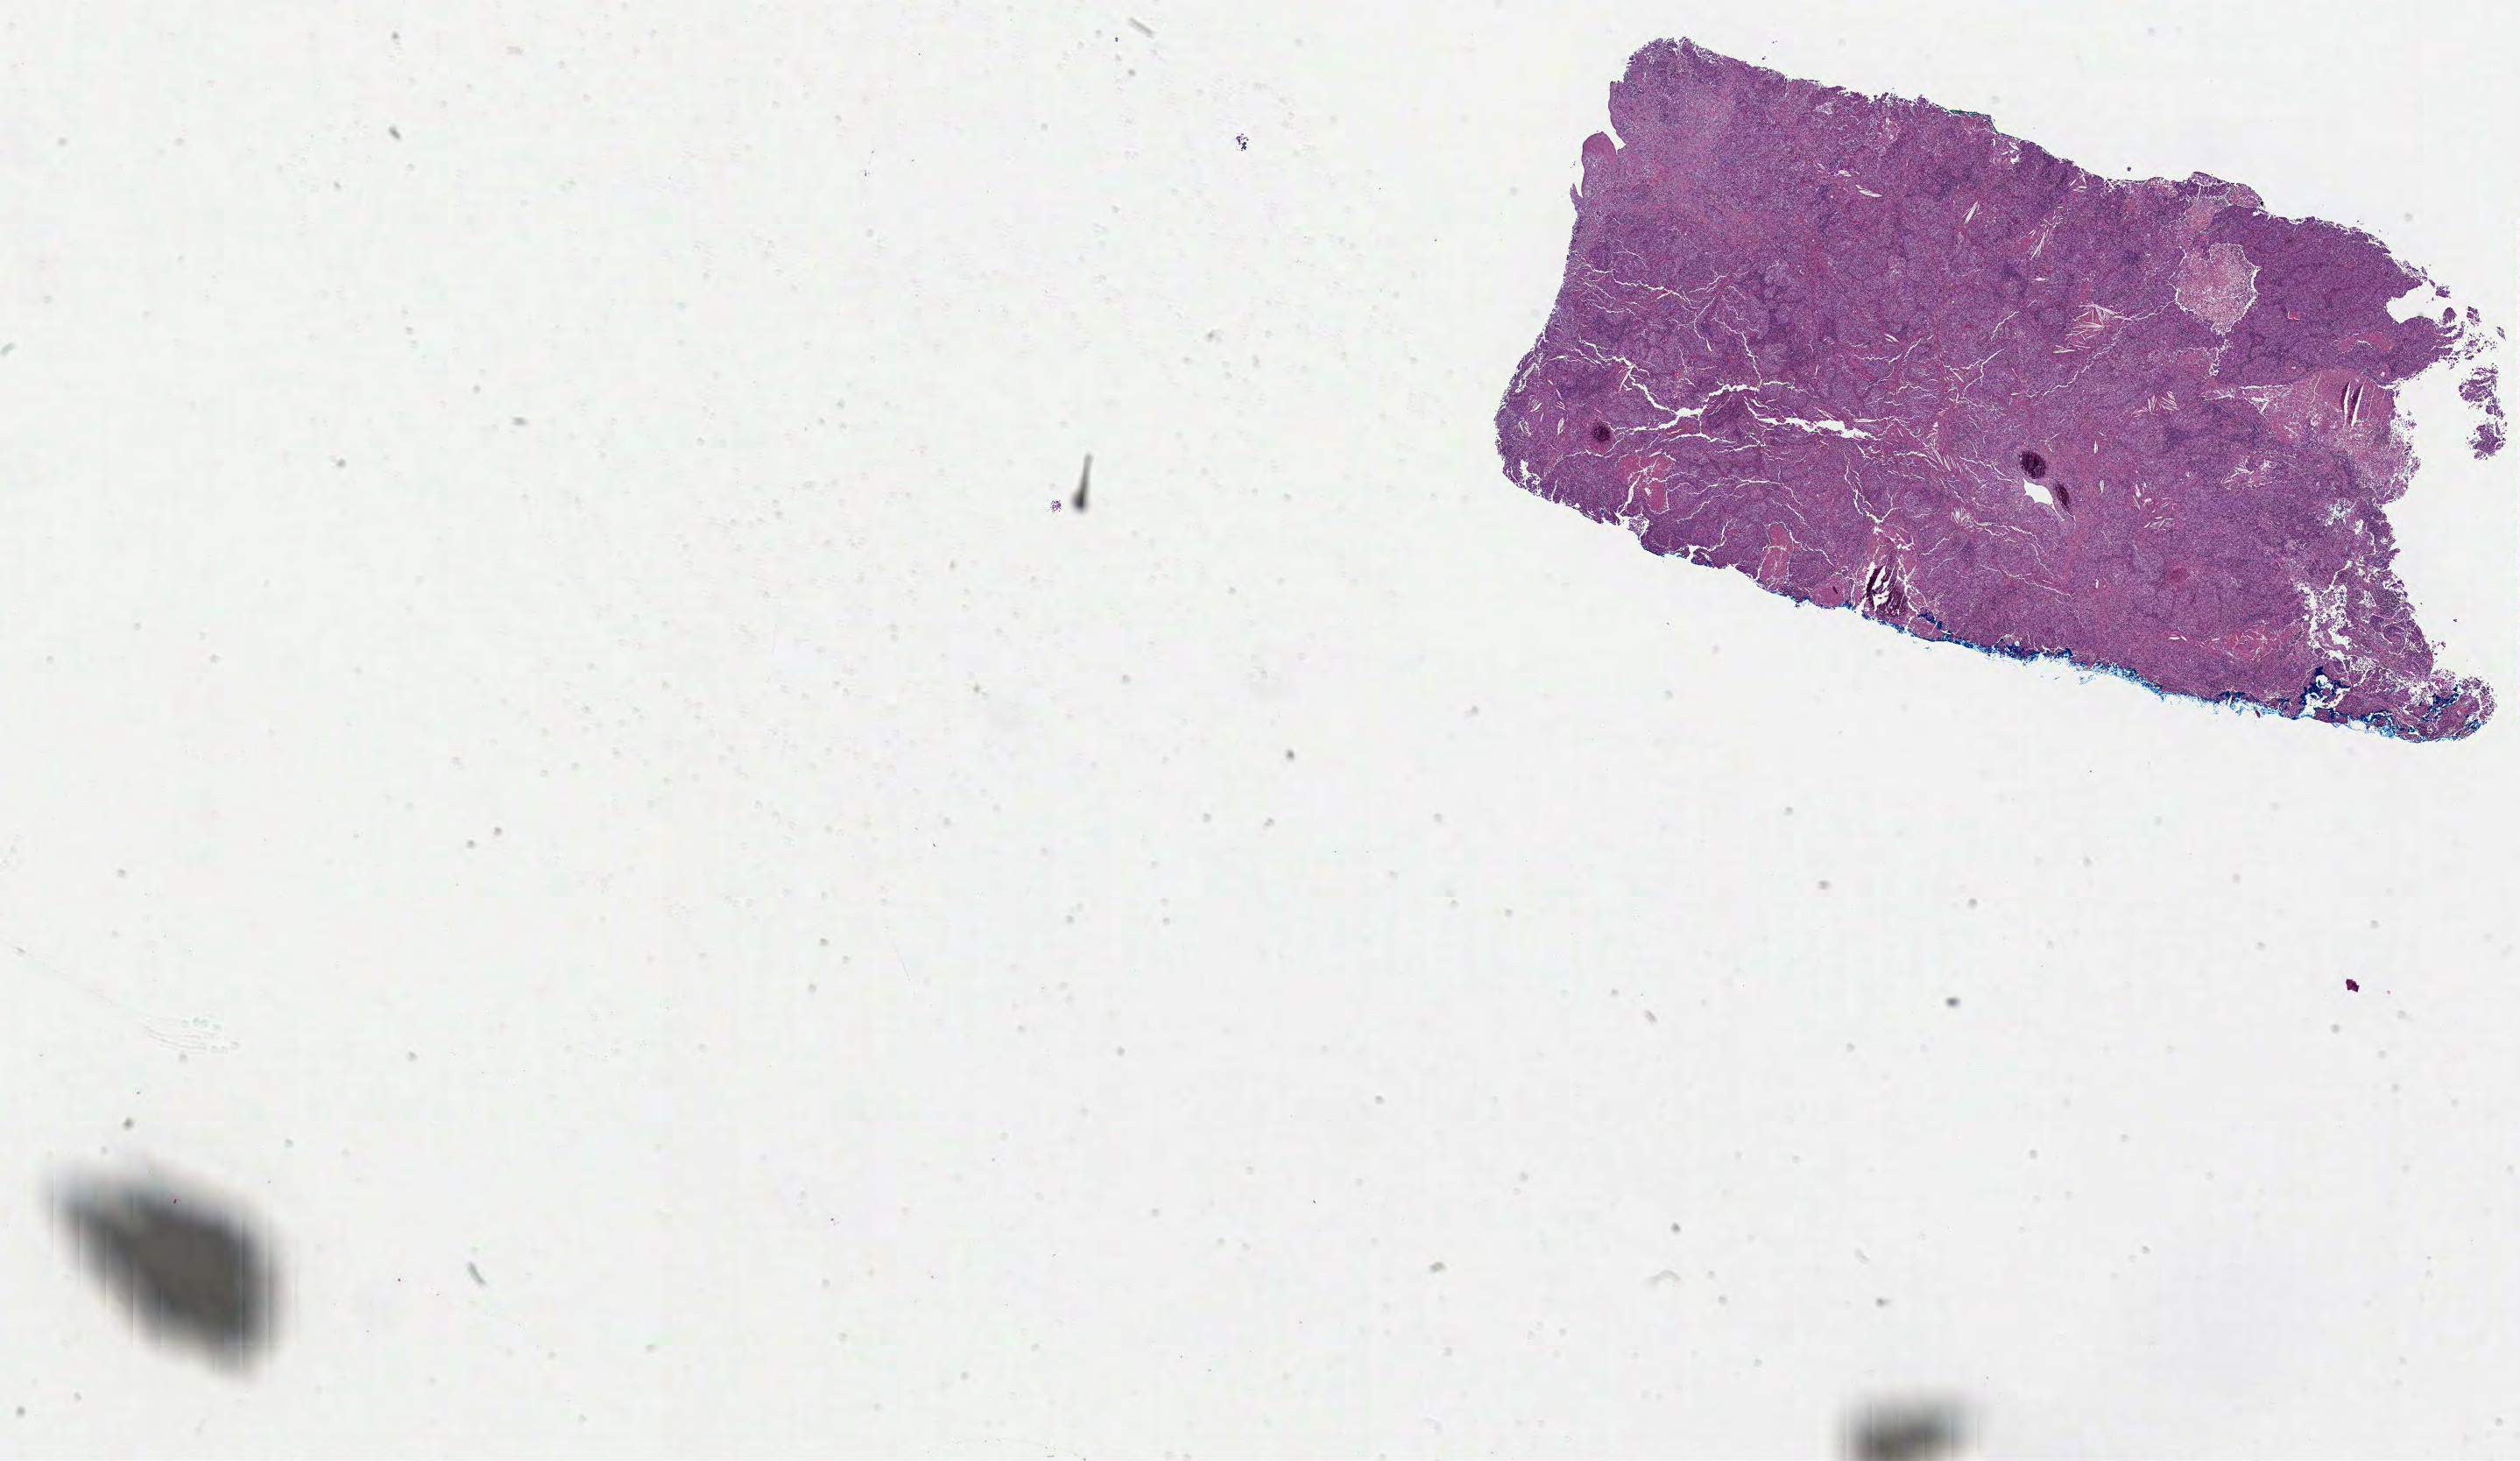
Hematoxylin and eosin (H&E) stained whole-slide image — low-resolution overview of the scanned area, about 23.2 x 13.5 mm (slide scanned at 40x); formalin-fixed paraffin-embedded (FFPE) diagnostic section; primary tumour sample from the lung. Female patient; age at initial diagnosis 73 years.
Diagnosis: Adenocarcinoma, NOS (upper lobe, lung).